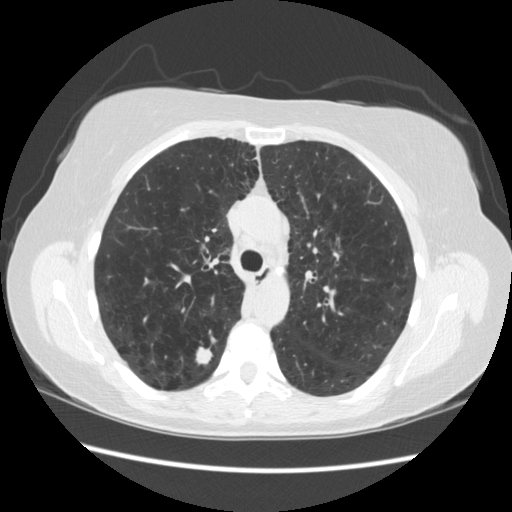
Low-dose screening chest CT, one axial slice. Slice 161 of 235 in the series (ordered by position). 120 kVp. Lung window (W 1500 / L -600 HU). 512 × 512 image matrix, field of view 360 × 360 mm.
Annotated regions visible in this slice (expert manual segmentation):
- lesion 1 (tumor, upper lobe of right lung): bounding box [x1, y1, x2, y2] px = [196, 342, 212, 364]